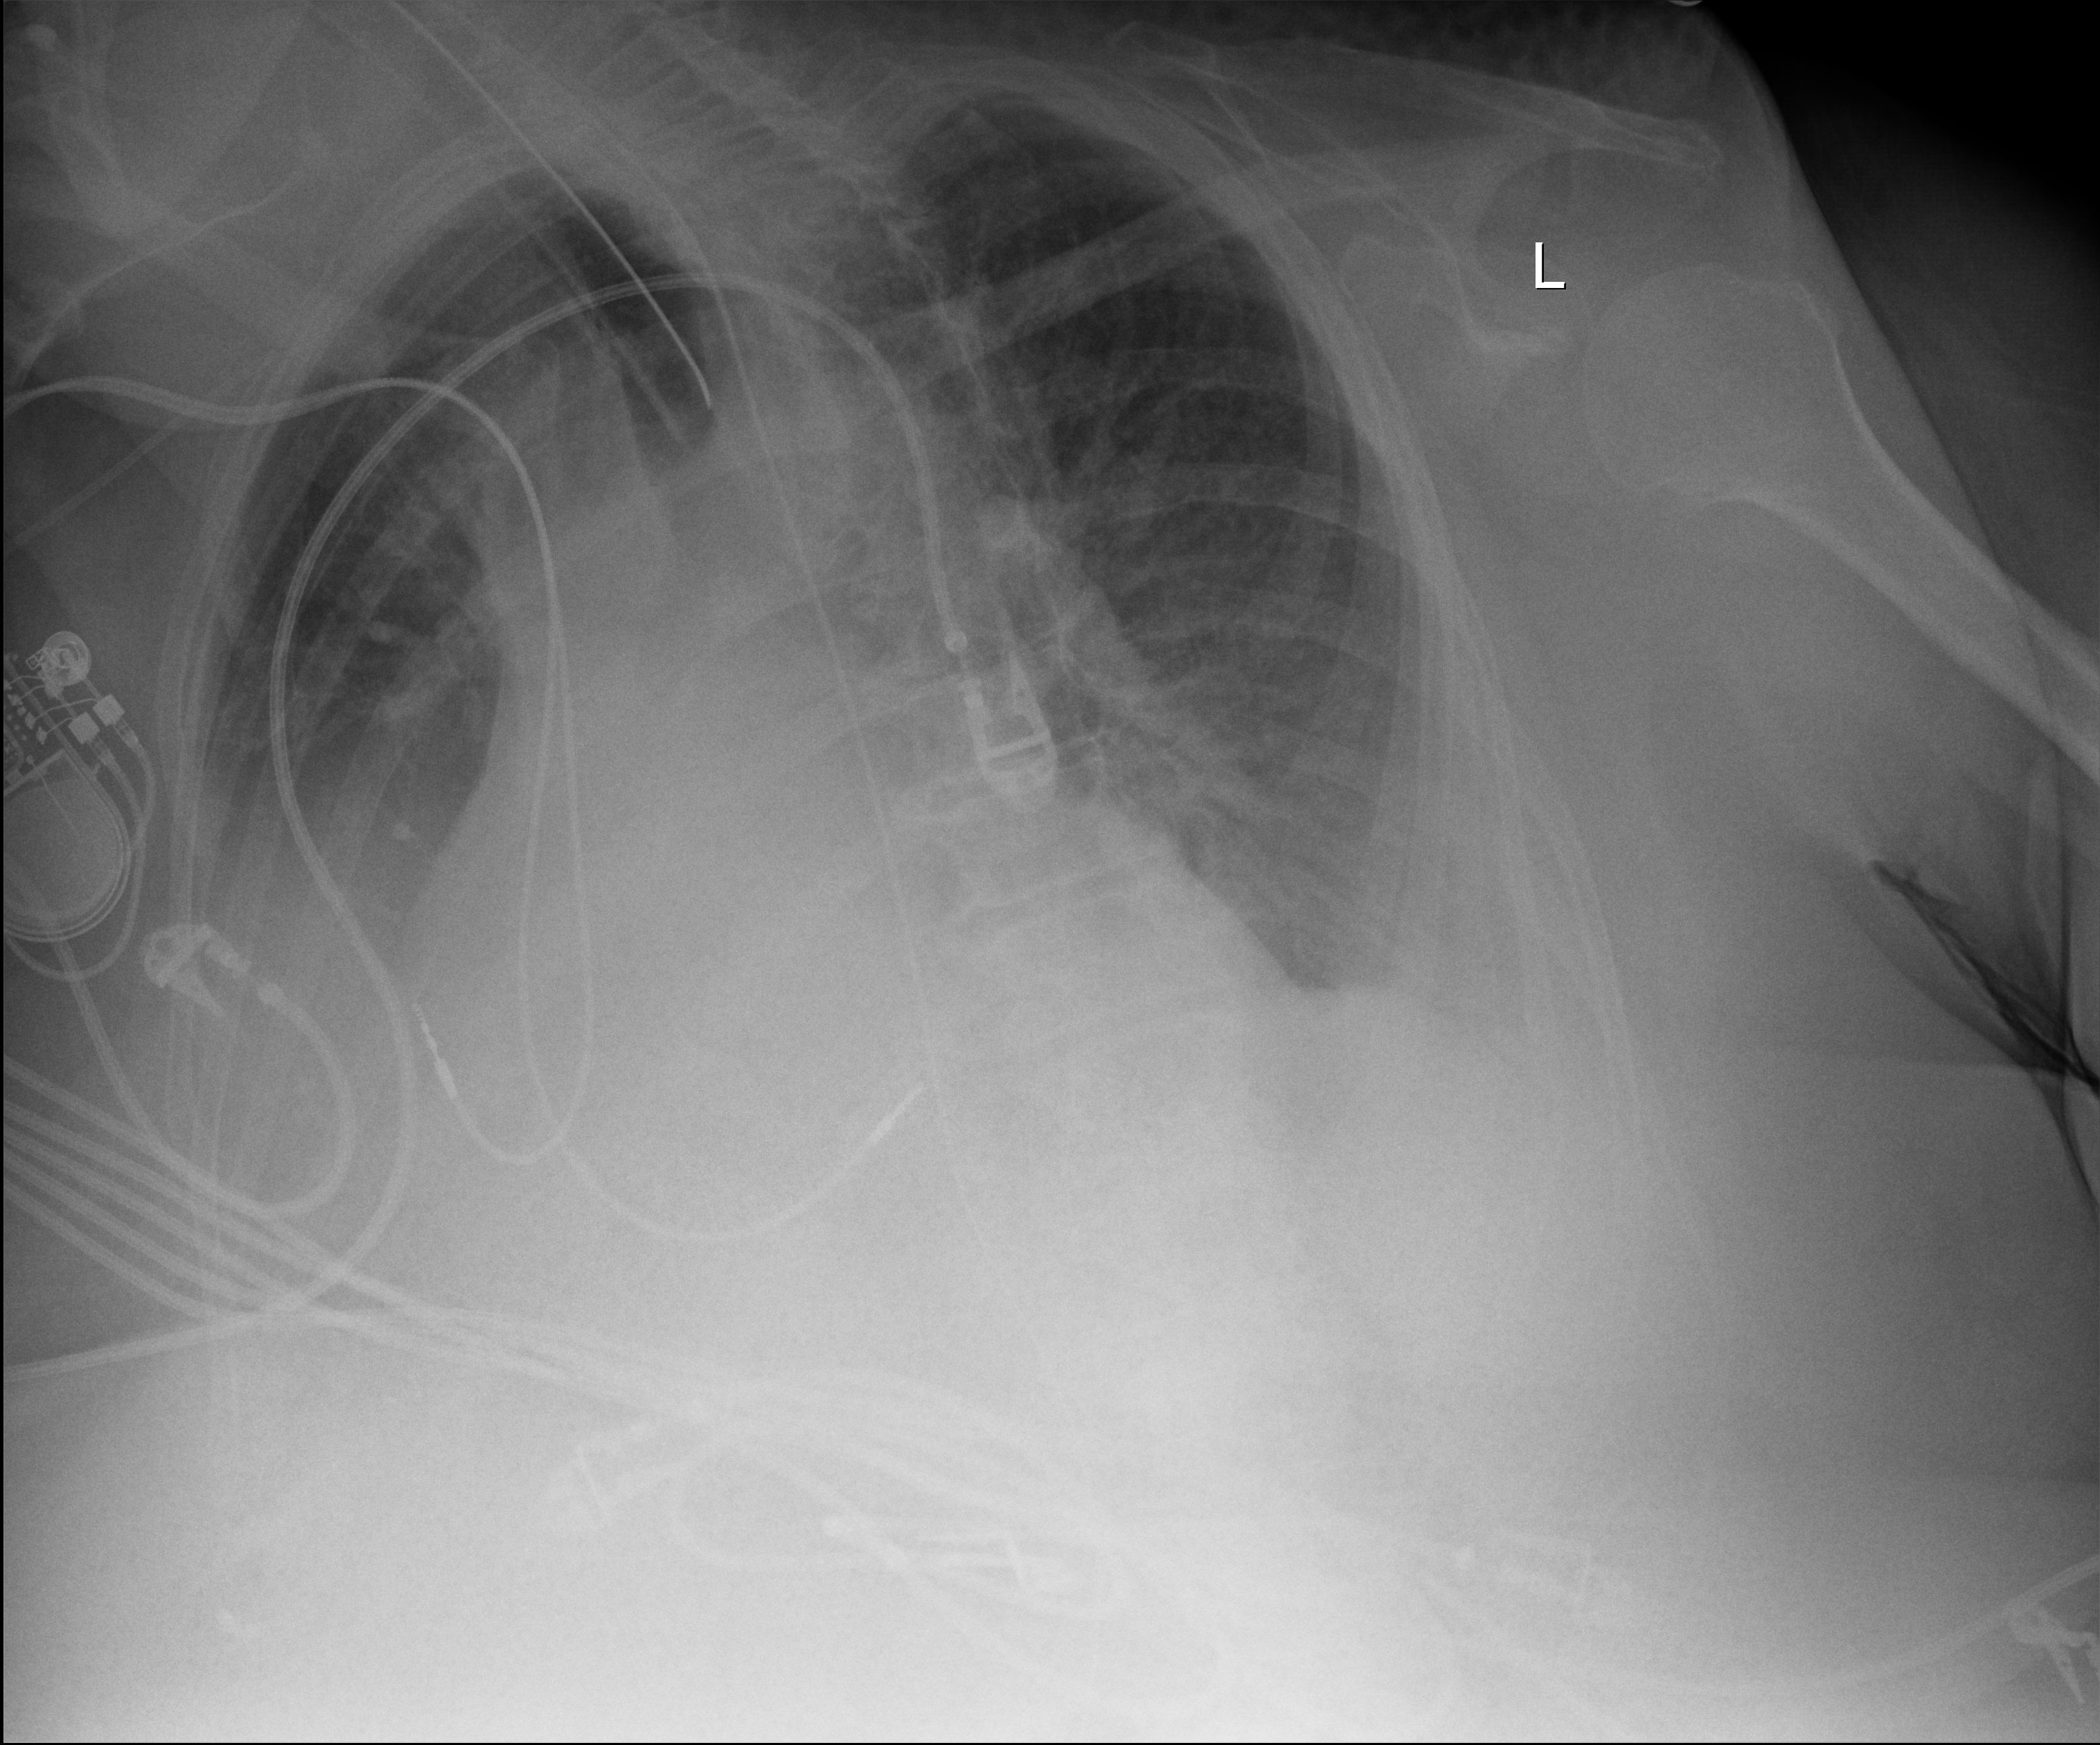
Bedside chest radiograph (digital radiography). Patient hospitalised with COVID-19; female, aged 75–90 years.
Admission-level facts for this patient (not findings on this image; timing relative to this image not recorded): mechanically ventilated during this hospital stay: yes; other chronic lung disease (admission record): yes; smoking status (admission record): former.